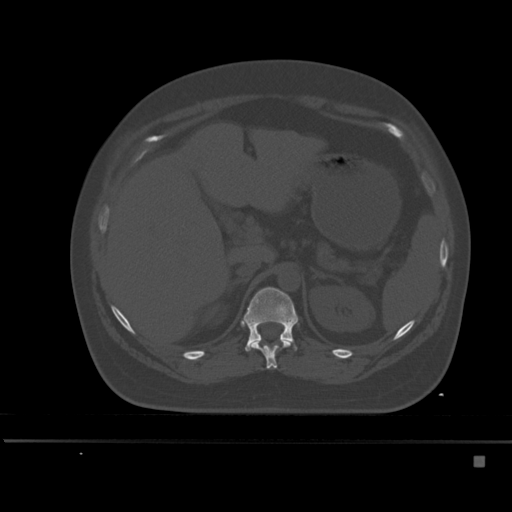
CT including the spine, one axial slice. Position 221 of 495 along the scan axis. Bone window (W 1800 / L 400 HU). 1.5 mm slice thickness. 512 × 512 image matrix, field of view 404 × 404 mm. Patient: female, 33 years. Case-level facts recorded for this patient, not image findings: primary cancer: breast; vertebrae with lytic lesions (as recorded): T1.
Annotated regions visible in this slice (semi-automatically segmented with operator editing):
- T11 vertebra: bounding box <249,340,292,369> (left, top, right, bottom; pixels)
- T12 vertebra: <242,287,298,351>